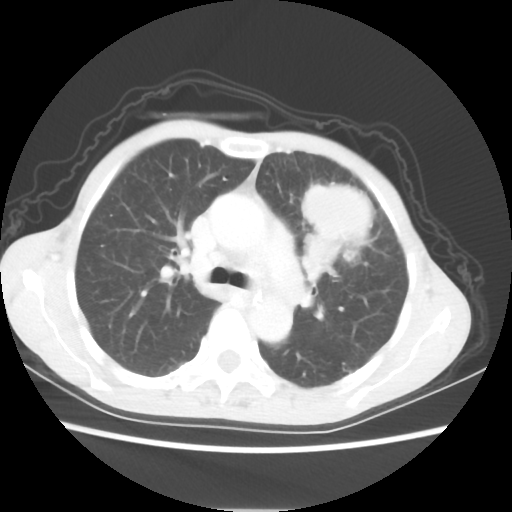
Chest CT, one axial slice; slice 39 of 56 in the series (ordered by position); reconstruction kernel STANDARD; 80 kVp; lung window (W 1500 / L -600 HU); 512 × 512 image matrix, field of view 331 × 331 mm. Female patient, age 60 years. Case-level facts recorded for this patient, not image findings: clinical TNM (as recorded): T4 N1 M0.
Outlined on this slice (rectangle marked by the reading radiologist):
- lung tumour (recorded histology: adenocarcinoma): bounding box (x1, y1, x2, y2) in pixels: (299, 177, 372, 286)